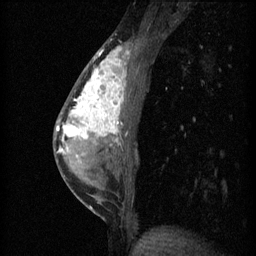
Breast MRI (dynamic contrast-enhanced), one sagittal slice; slice 25 of 60 in the series (ordered by position); 3 images stored at this slice position (order not interpretable as contrast timing); 1.5 T; TE 4.2 ms, TR 11 ms; 2 mm slice thickness; 256 × 256 image matrix. Patient: female, 40 years.
Annotated regions visible in this slice (semi-automatic segmentation, software-assisted and operator-edited):
- analysis volume of interest (the breast-tissue region the enhancement analysis was run in; not a lesion): bounding box (x1, y1, x2, y2) in pixels: (55, 42, 136, 203)
- tumour enhancement mask (voxels above the 70 % enhancement threshold inside the analysis volume of interest): (57, 48, 130, 155)